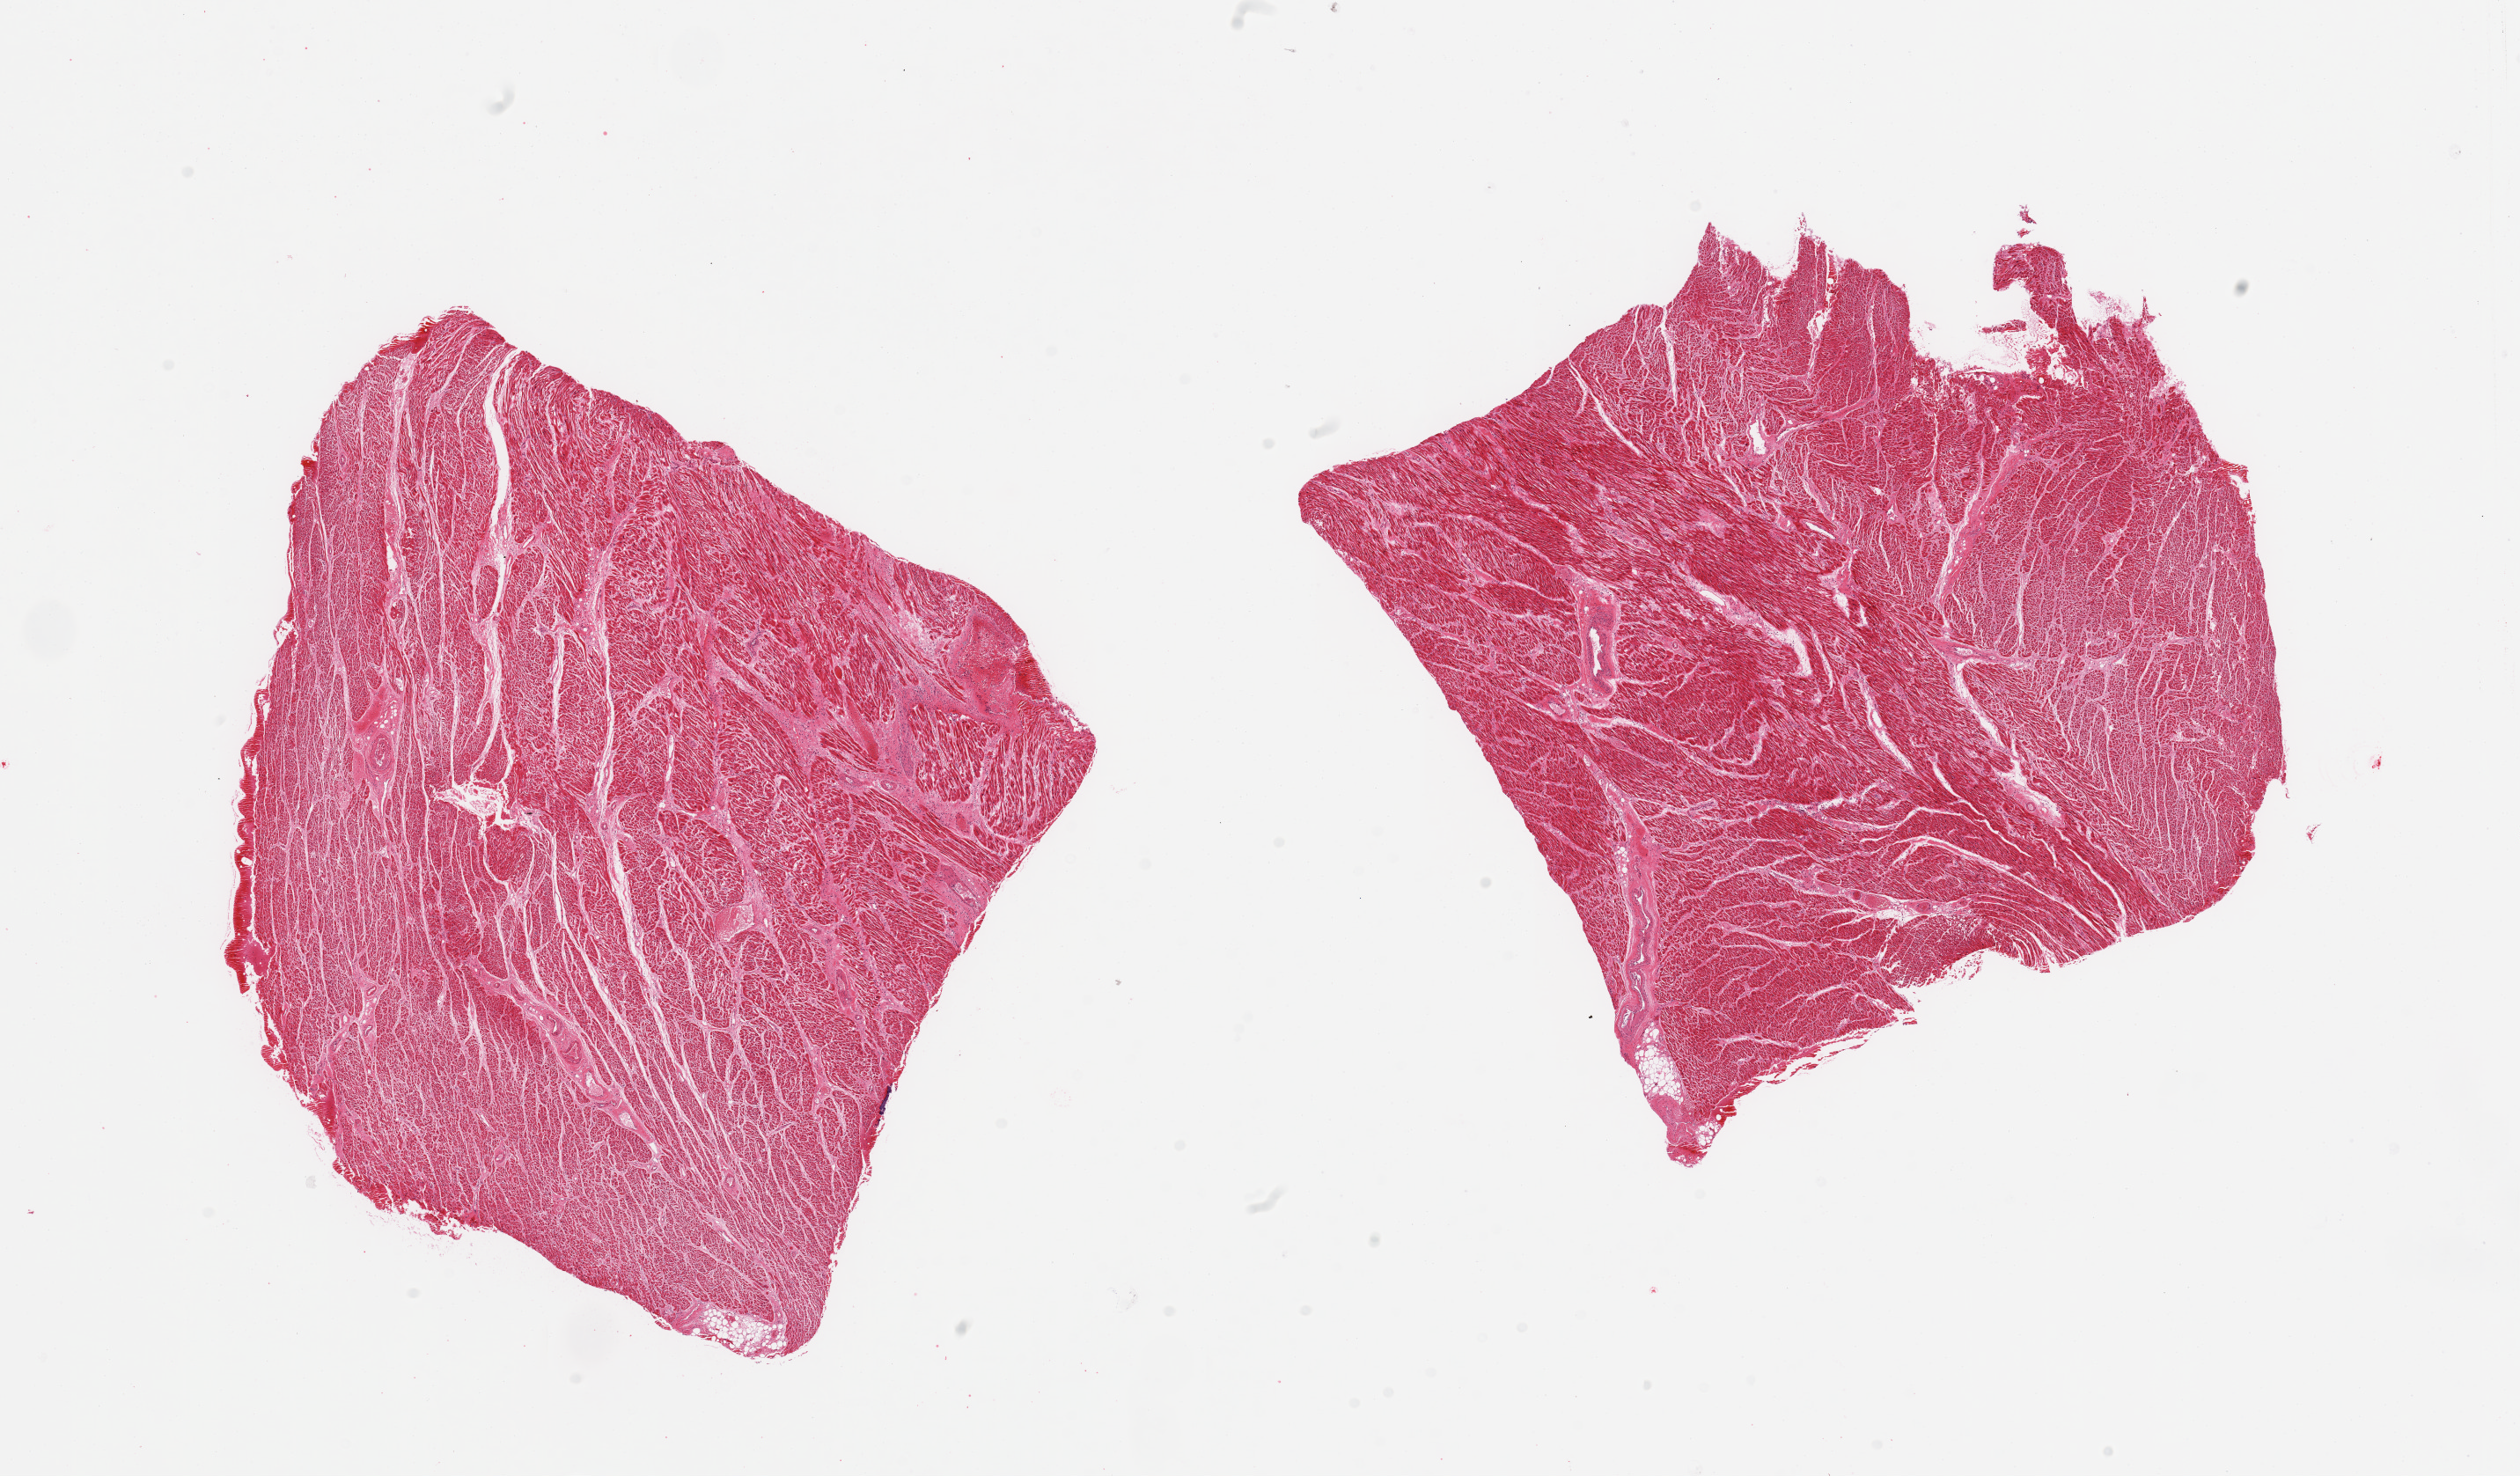
H&E whole-slide image, whole scanned area (about 22.6 x 13.3 mm) shown as a low-resolution overview. PAXgene-fixed paraffin-embedded (PFPE) section. Sampled site (target tissue): heart. Donor tissue sample. Male donor.
* reviewer comment on this tissue sample: 2 pieces; scattered foci (10%) of hypereosinophilia, edema, and polys, with other foci of fibrosis consistent with recent and old infarcts